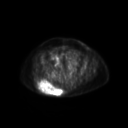
FDG PET of an extremity soft-tissue mass (from a PET/CT study), one axial slice; position 68 of 267 along the scan axis; 3.27 mm slice thickness; 128 × 128 image matrix, field of view 600 × 600 mm. Patient: female, 60 years. From the clinical record (not read from this slice): histological type: spindle cell suggestive of myxofibrosarcoma; grade: intermediate; site of the primary tumour: right buttock.
Structures marked on this image (expert contour drawn on MRI and transferred to this co-registered scan by the dataset authors):
- gross tumour volume (mass): bounding box <37,79,63,96> (left, top, right, bottom; pixels)